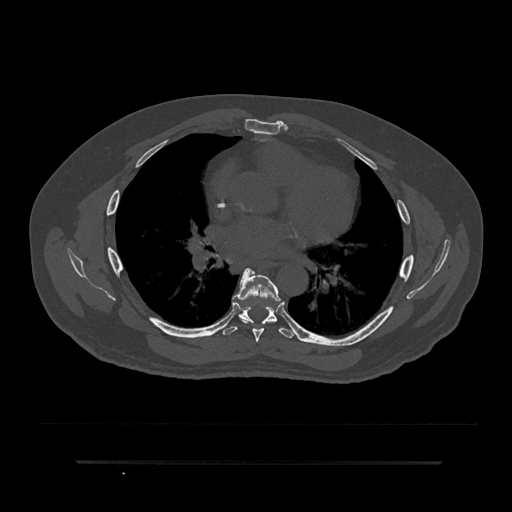
CT including the spine, one axial slice; position 505 of 797 along the scan axis; reconstruction kernel Br40s/3; 120 kVp; bone window (W 1800 / L 400 HU); 512 × 512 image matrix, field of view 464 × 464 mm. Male patient, age 59 years. Case-level facts recorded for this patient, not image findings: primary cancer: bile ducts; vertebrae with lytic lesions (as recorded): T10.
Outlined on this slice (semi-automatically segmented with operator editing):
- T6 vertebra: box from (x=232, y=268) to (x=281, y=343) px
- T7 vertebra: (x=223, y=268)–(x=295, y=338)